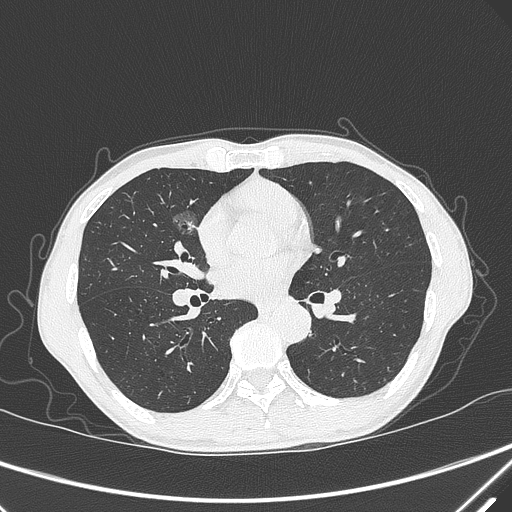
Chest CT, one axial slice; slice 167 of 339 in the series (ordered by position); 120 kVp; lung window (W 1500 / L -600 HU); 512 × 512 image matrix, field of view 350 × 350 mm. Male patient, age 67 years. Case-level facts recorded for this patient, not image findings: clinical TNM (as recorded): T1c N0 M0.
Annotated regions visible in this slice (rectangle marked by the reading radiologist):
- lung tumour (recorded histology: adenocarcinoma): bounding box (x1, y1, x2, y2) in pixels: (169, 204, 203, 241)